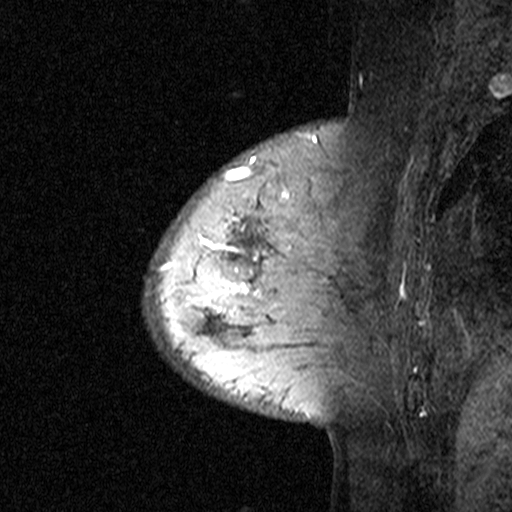
Breast MRI (dynamic contrast-enhanced), one sagittal slice; position 9 of 44 along the scan axis; dynamic contrast-enhanced study with each time point stored as its own series, time point 3 of 4 at this slice position (ordered by acquisition time); 1.5 T; TE 4.5 ms, TR 11 ms; 3 mm slice thickness; 512 × 512 image matrix. Female patient, age 65 years. From the clinical record (not read from this slice): setting: breast cancer imaged before/during neoadjuvant chemotherapy; receptor status: HER2-positive.
Structures marked on this image (semi-automatic segmentation, software-assisted and operator-edited):
- analysis volume of interest (the breast-tissue region the enhancement analysis was run in; not a lesion): bounding box <182,190,353,361> (left, top, right, bottom; pixels)
- tumour enhancement mask (voxels above the 90 % enhancement threshold inside the analysis volume of interest): <202,228,259,314>